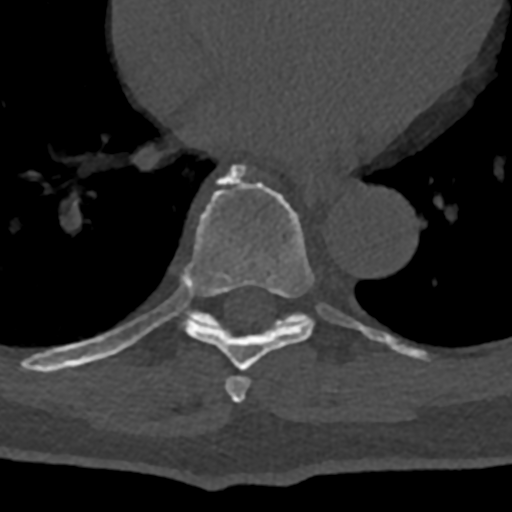
CT including the spine, one axial slice; slice 699 of 797 in the series (ordered by position); bone window (W 1800 / L 400 HU); 512 × 512 image matrix. Patient: male, 74 years. From the clinical record (not read from this slice): primary cancer: renal; vertebrae with lytic lesions (as recorded): T10, L1, L2, L3, L4, L5.
Annotated regions visible in this slice (semi-automatic segmentation, software-assisted and operator-edited):
- T7 vertebra: bounding box [x1, y1, x2, y2] px = [225, 375, 251, 403]
- T8 vertebra: [70, 165, 385, 371]
- T9 vertebra: [173, 288, 430, 361]